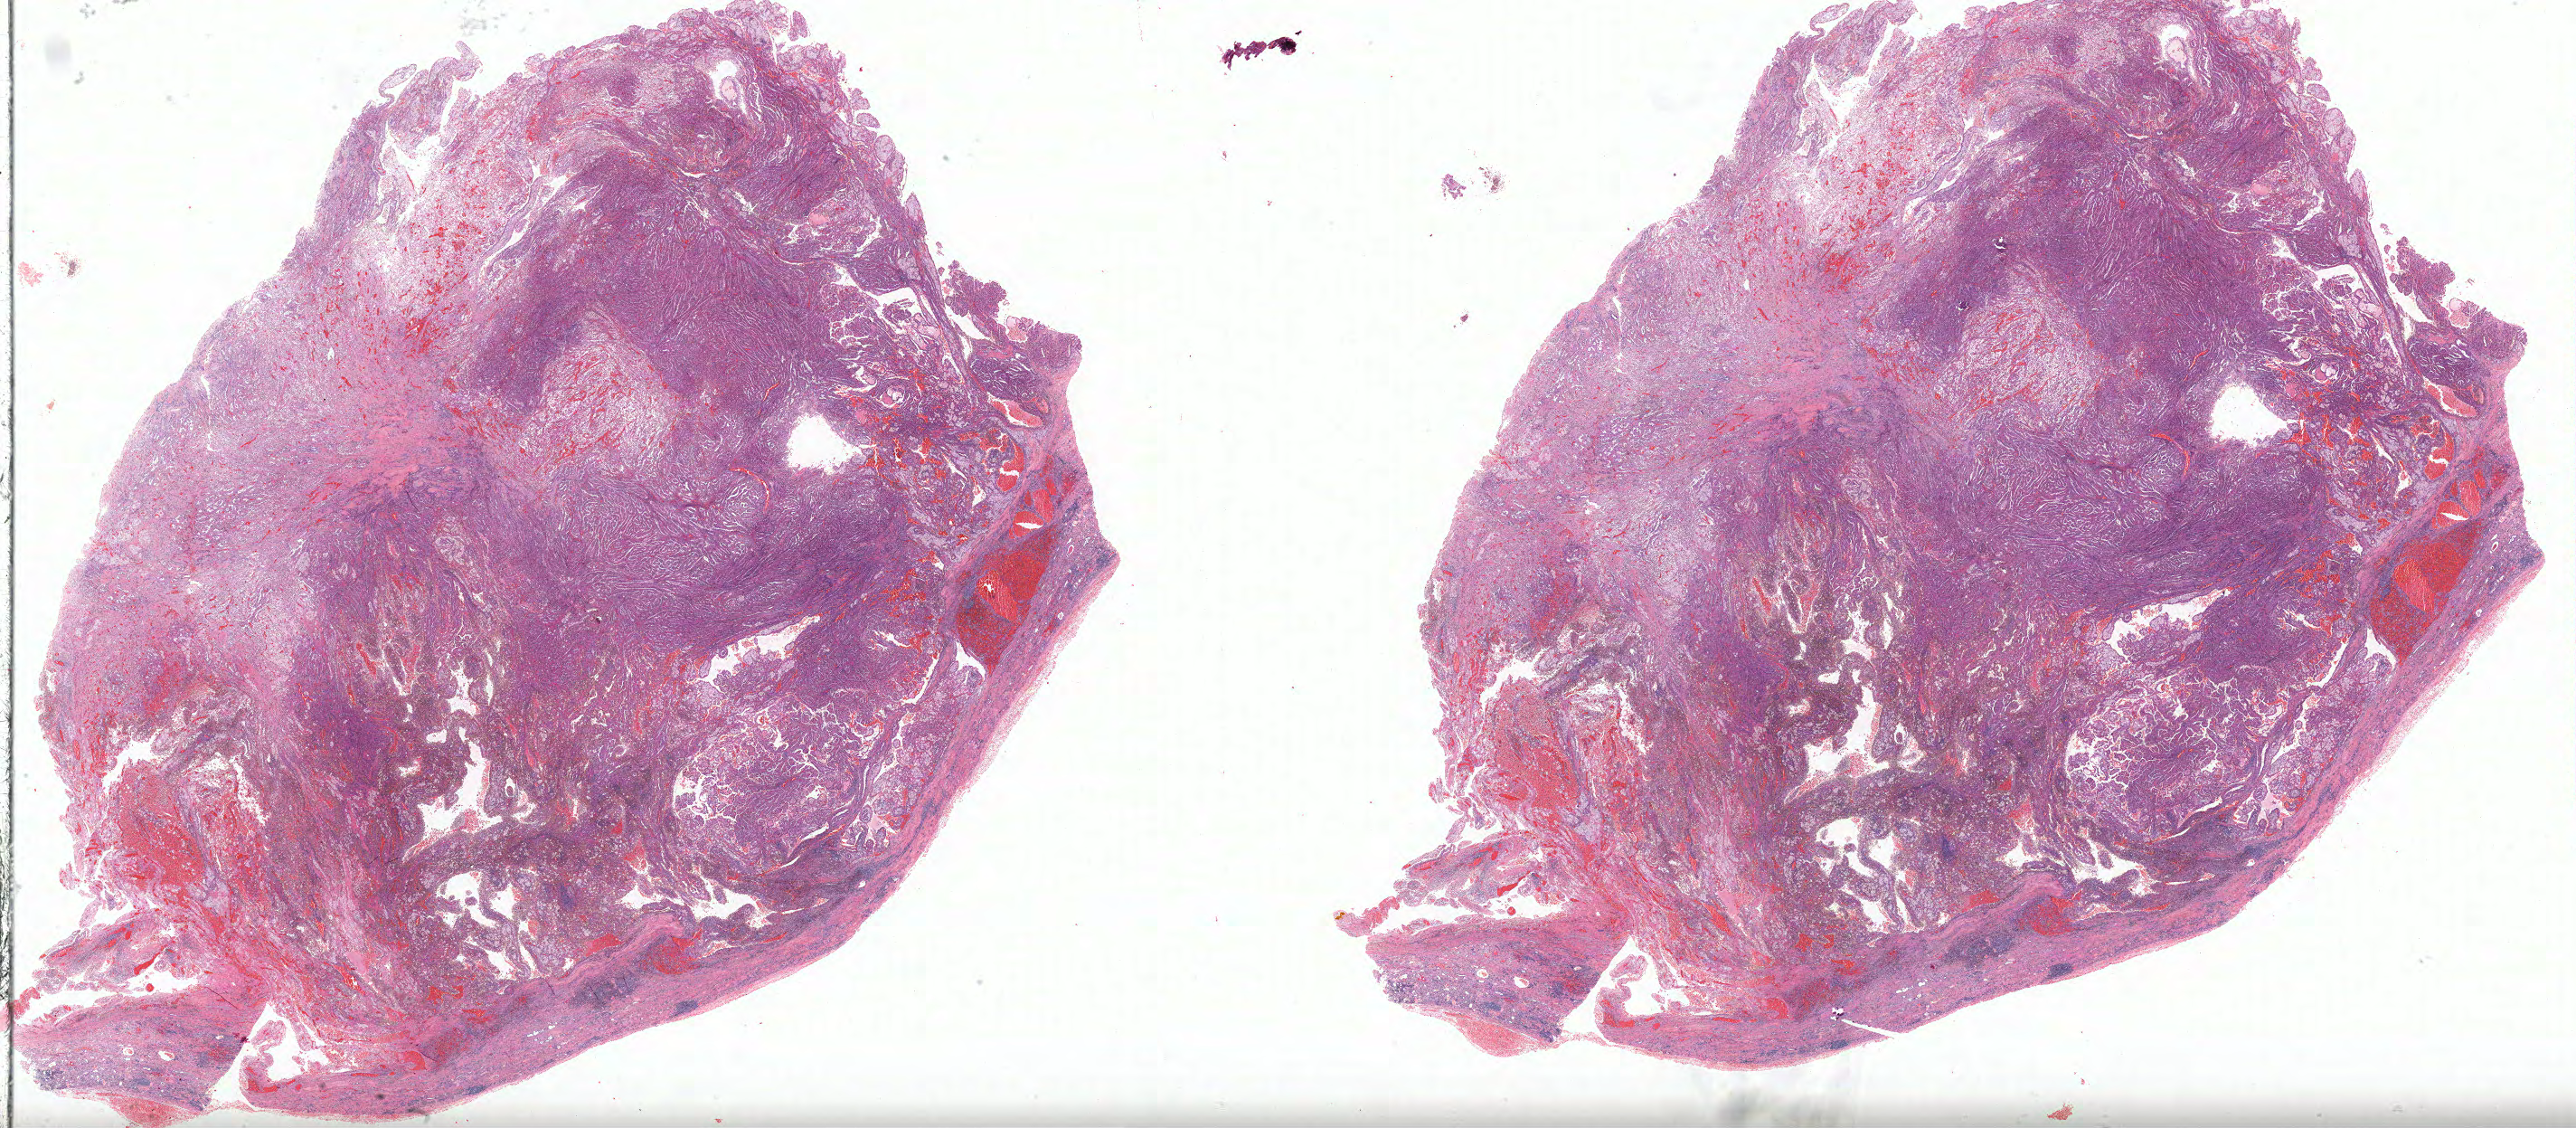
Digitized Hematoxylin and eosin (H&E) stained tissue section (whole slide), shown as a low-resolution overview of the whole scanned area (about 45.6 x 19.9 mm, from a 40x scan), formalin-fixed paraffin-embedded (FFPE) diagnostic section, primary tumour sample from the kidney. Male, age 78 years at initial diagnosis.
Diagnosis: Papillary adenocarcinoma, NOS. AJCC pathologic stage: I (5th edition). Laterality: left.